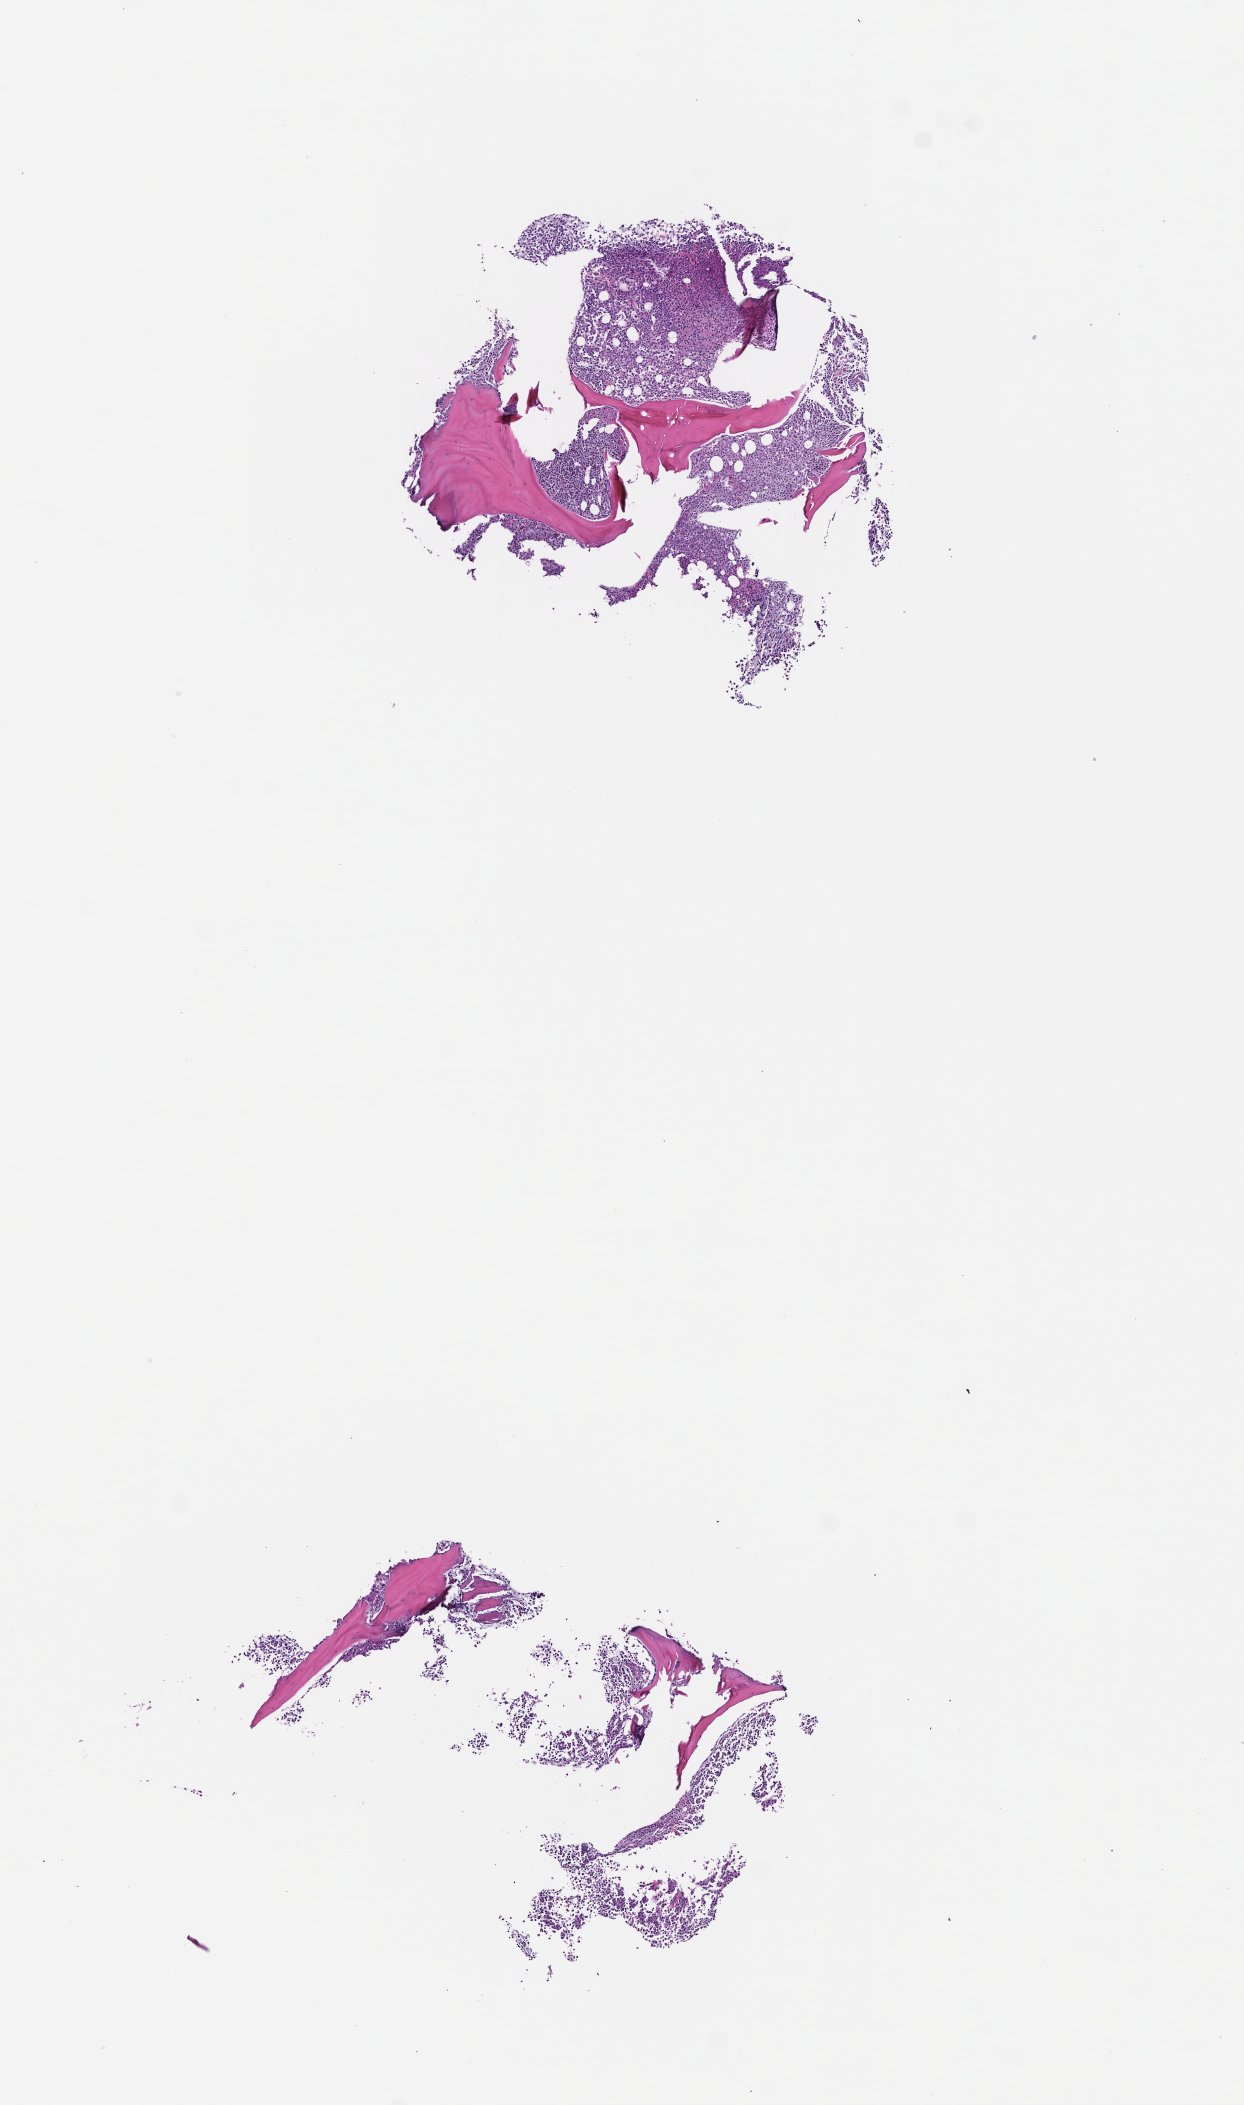
Haematoxylin and eosin whole-slide image, low-resolution overview of the scanned area, about 5.0 x 8.5 mm. FFPE section. Site: bone marrow. Collected at baseline (before treatment). Patient: male.
This section: primary tumor. Diagnosis: Plasma Cell Myeloma.